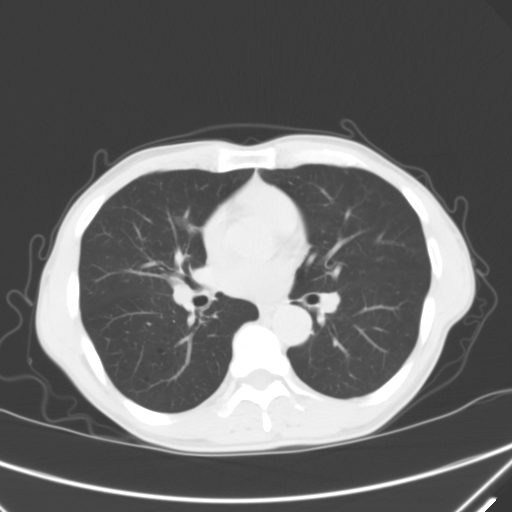
Chest CT, one axial slice; lung window (W 1500 / L -600 HU); 512 × 512 image matrix, field of view 350 × 350 mm. Patient: male, 67 years. From the clinical record (not read from this slice): clinical TNM (as recorded): T1c N0 M0; histopathological grade: G1-2.
Structures marked on this image (rectangle marked by the reading radiologist):
- lung tumour (recorded histology: adenocarcinoma): bounding box <172,208,195,243> (left, top, right, bottom; pixels)